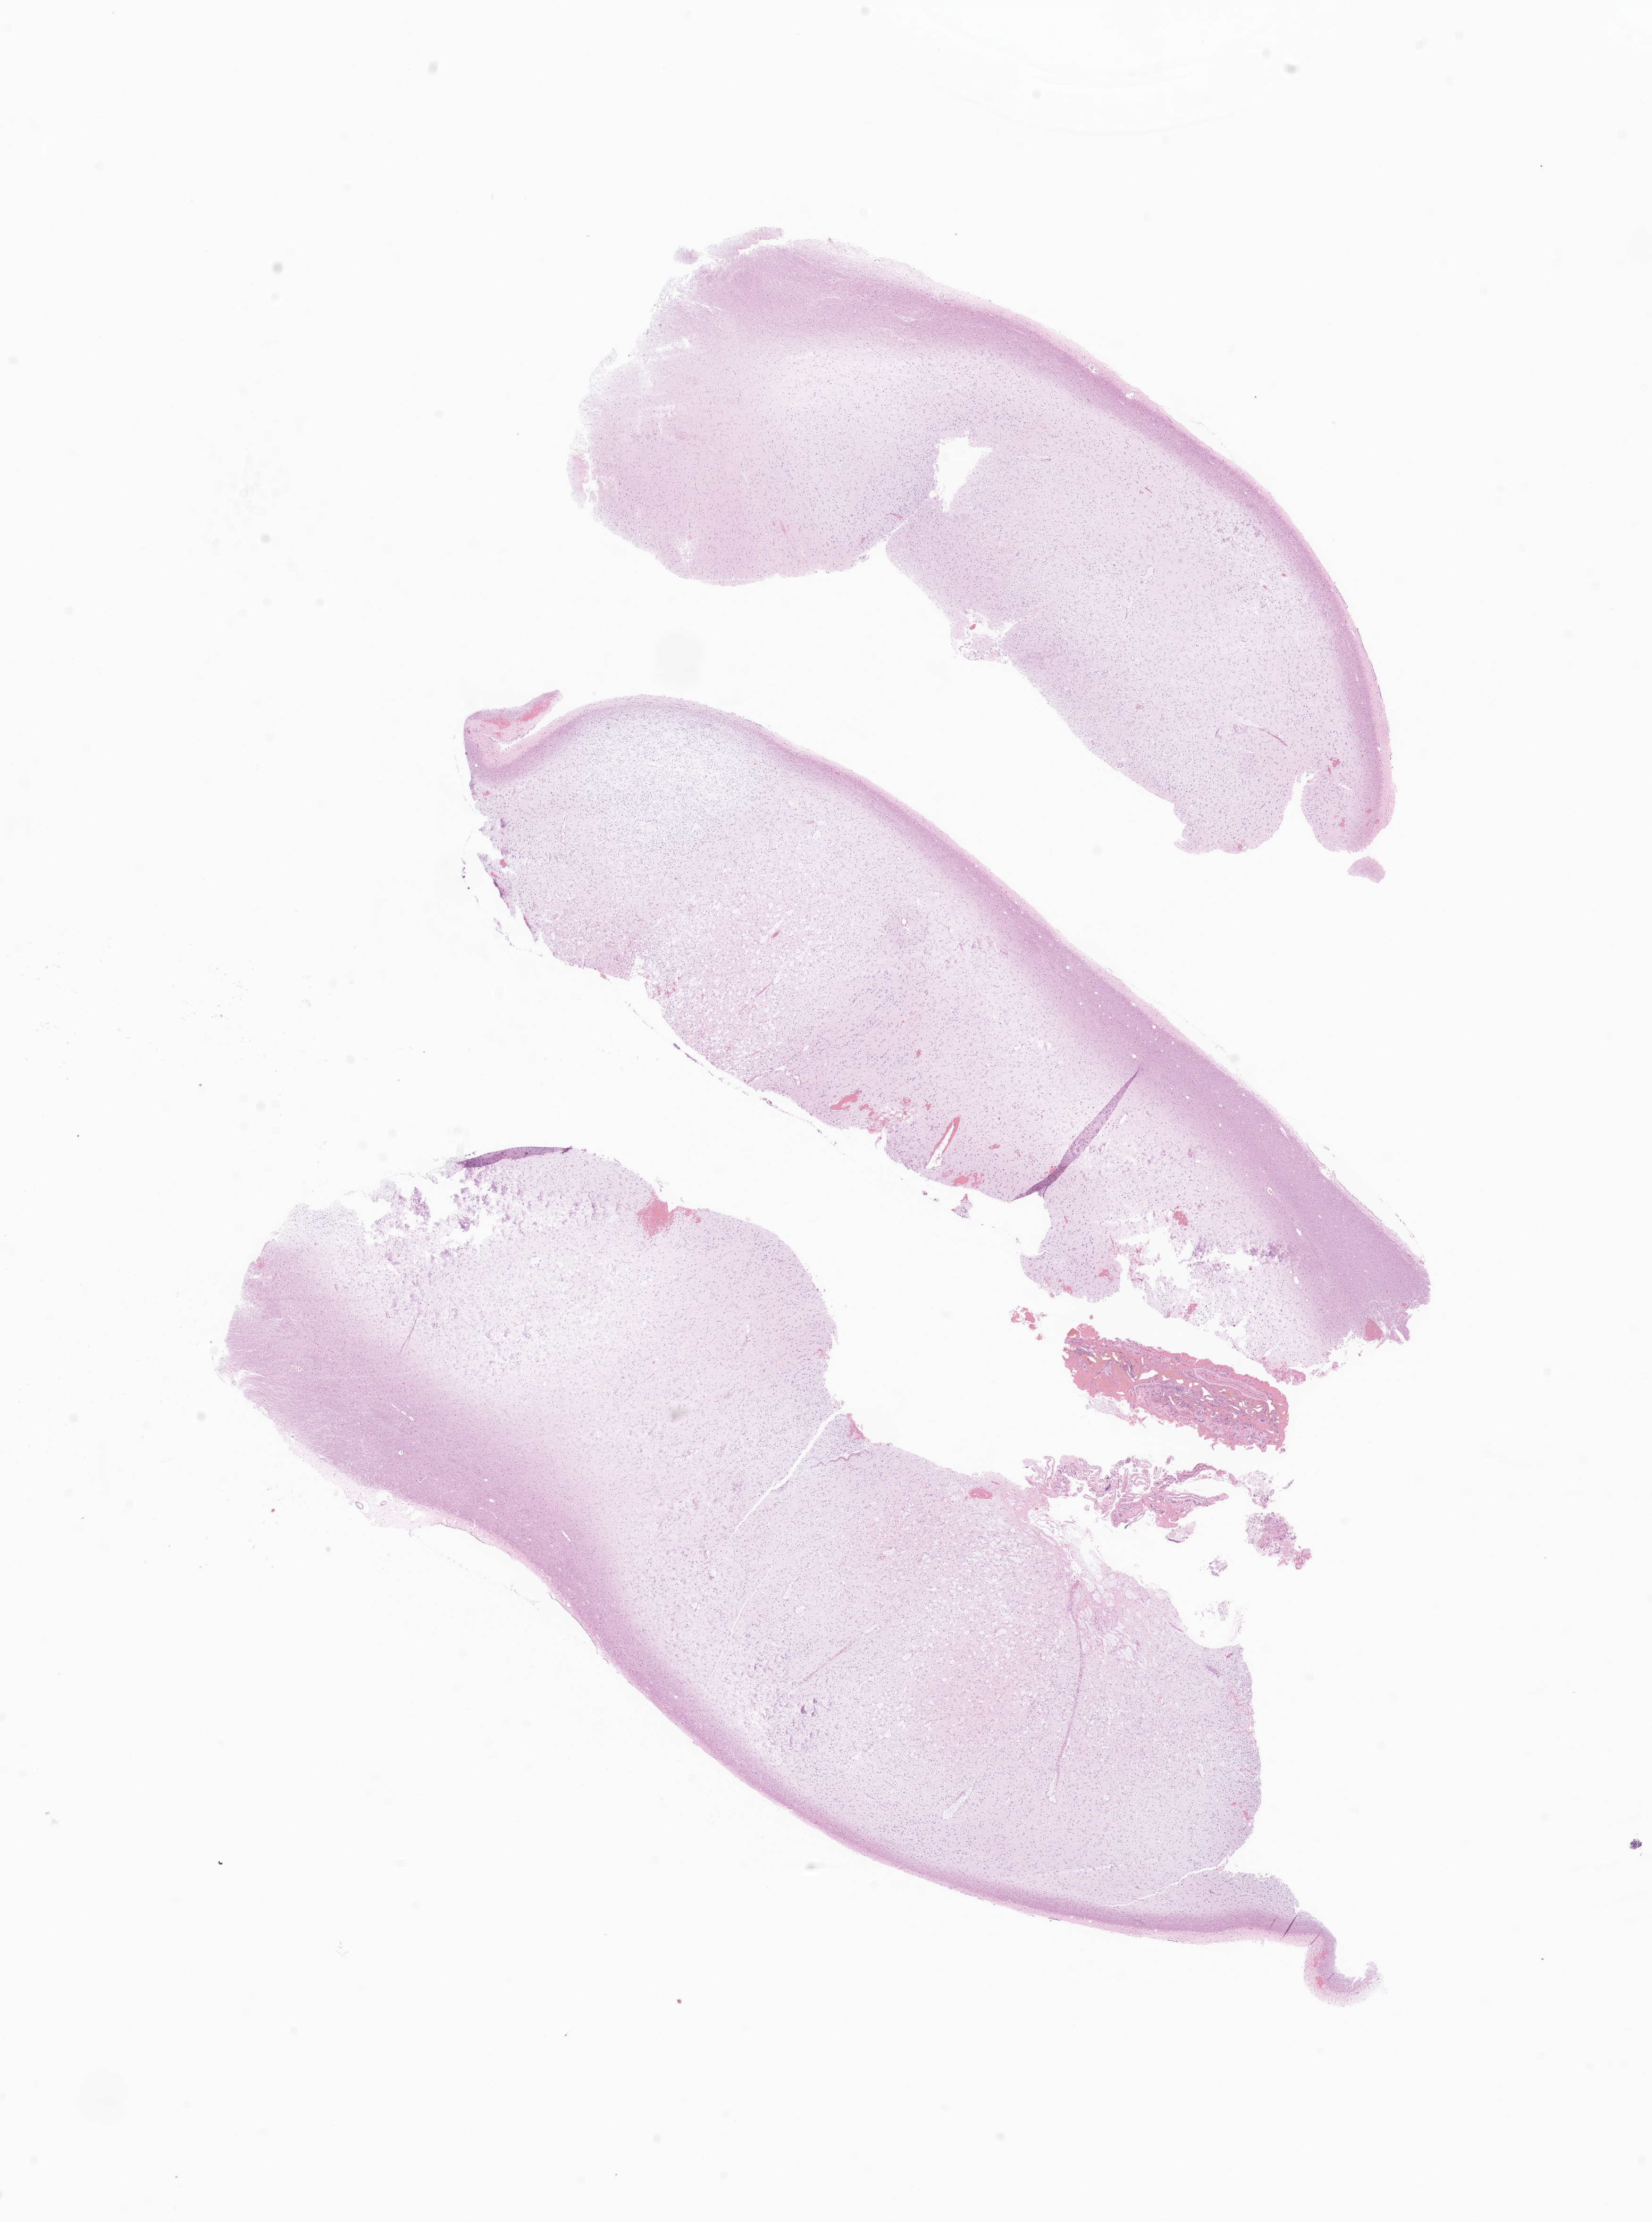
H&E whole-slide image of tumor tissue from the occipital lobe, a low-resolution overview of the entire scanned area, about 14.8 x 19.9 mm, formalin-fixed, paraffin-embedded (FFPE) tissue. Patient female; age 53 months (4 years 5 months).
Diagnosis (ICD-O-3 morphology term): Dysembryoplastic neuroepithelial tumor.